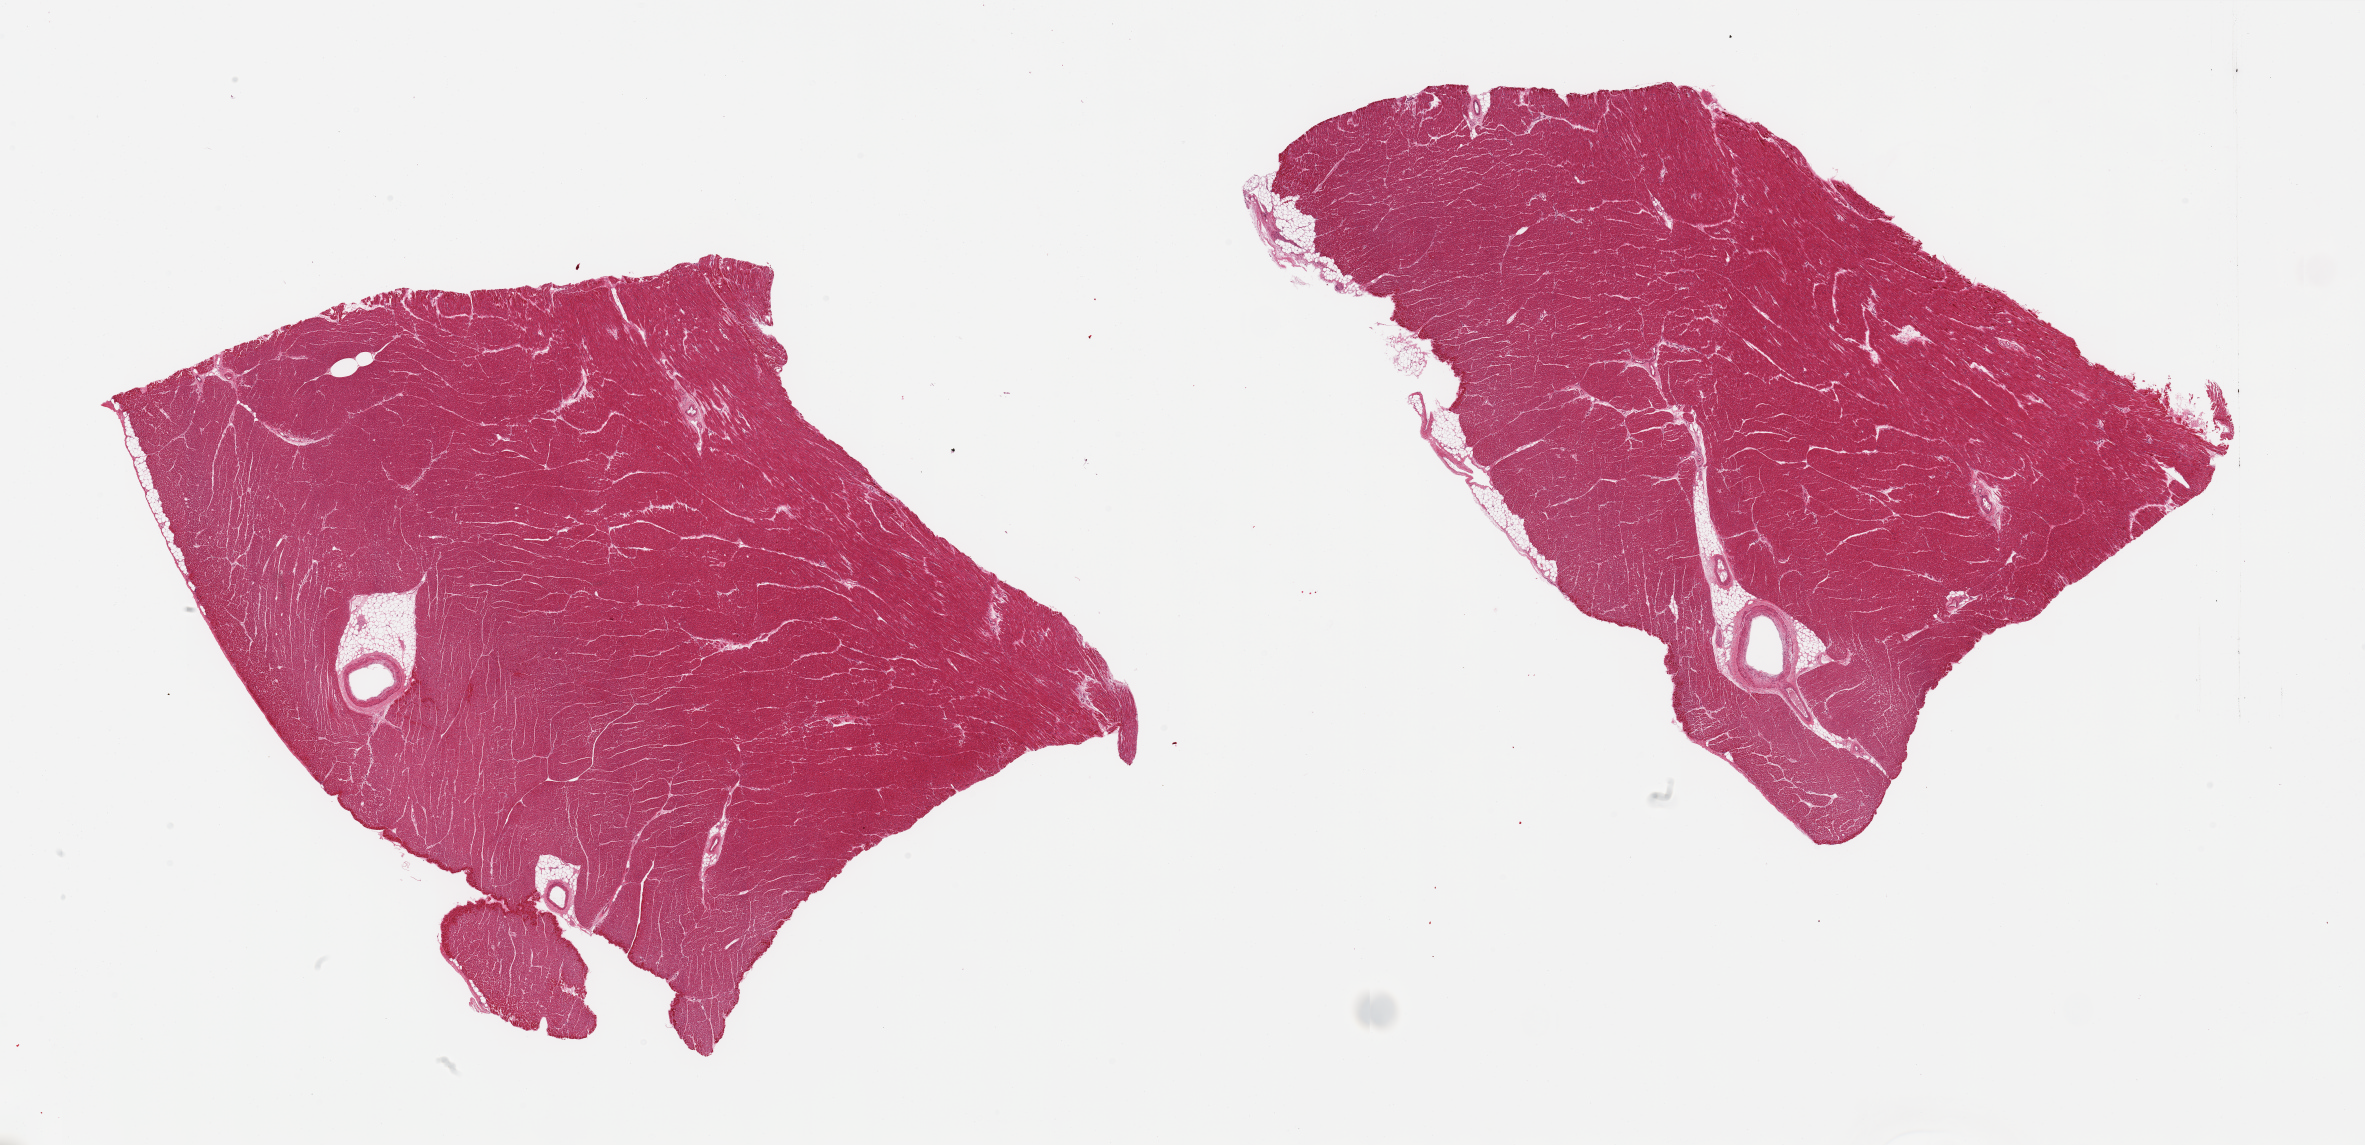
Hematoxylin and eosin (H&E) whole-slide image, low-resolution overview of the scanned area, about 37.4 x 18.1 mm (from a 20x scan). PAXgene-fixed, paraffin-embedded tissue. Sampled site (target tissue): heart. Tissue donor sample. Female donor.
Reviewer comment on this tissue sample: 2 pieces, minimal interstitial fibrosis.